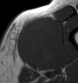
MRI of an extremity soft-tissue mass, one axial slice; position 21 of 43 along the scan axis; MR volume resampled by the dataset authors to the PET/CT grid (not the native acquisition matrix); 3.27 mm slice thickness; 78 × 83 image matrix, field of view 76 × 81 mm. Male patient. Case-level facts recorded for this patient, not image findings: histological type: pleiomorphic leiomyosarcoma; grade: high; site of the primary tumour: left thigh.
Structures marked on this image (expert contour drawn on MRI and transferred to this co-registered scan by the dataset authors):
- gross tumour volume including surrounding oedema: bounding box <15,17,60,66> (left, top, right, bottom; pixels)
- gross tumour volume (mass): <15,17,57,66>